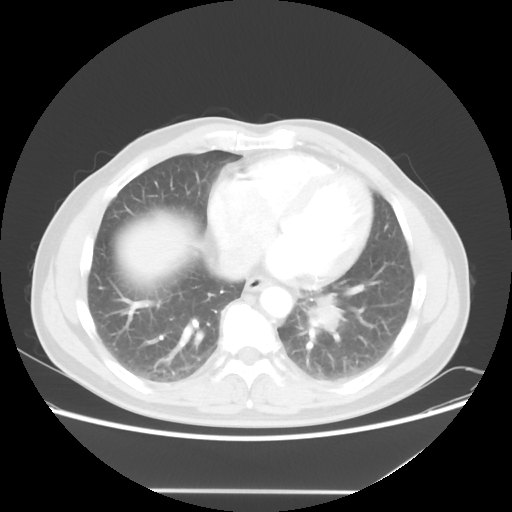
Chest CT, one axial slice. Position 21 of 56 along the scan axis. Lung window (W 1500 / L -600 HU). 5 mm slice thickness. 512 × 512 image matrix, field of view 385 × 385 mm. Male patient, age 61 years. Case-level facts recorded for this patient, not image findings: clinical TNM (as recorded): T1c N0 M0; histopathological grade: G3.
Annotated regions visible in this slice (rectangle marked by the reading radiologist):
- lung tumour (recorded histology: adenocarcinoma): bounding box <298,289,357,345> (left, top, right, bottom; pixels)